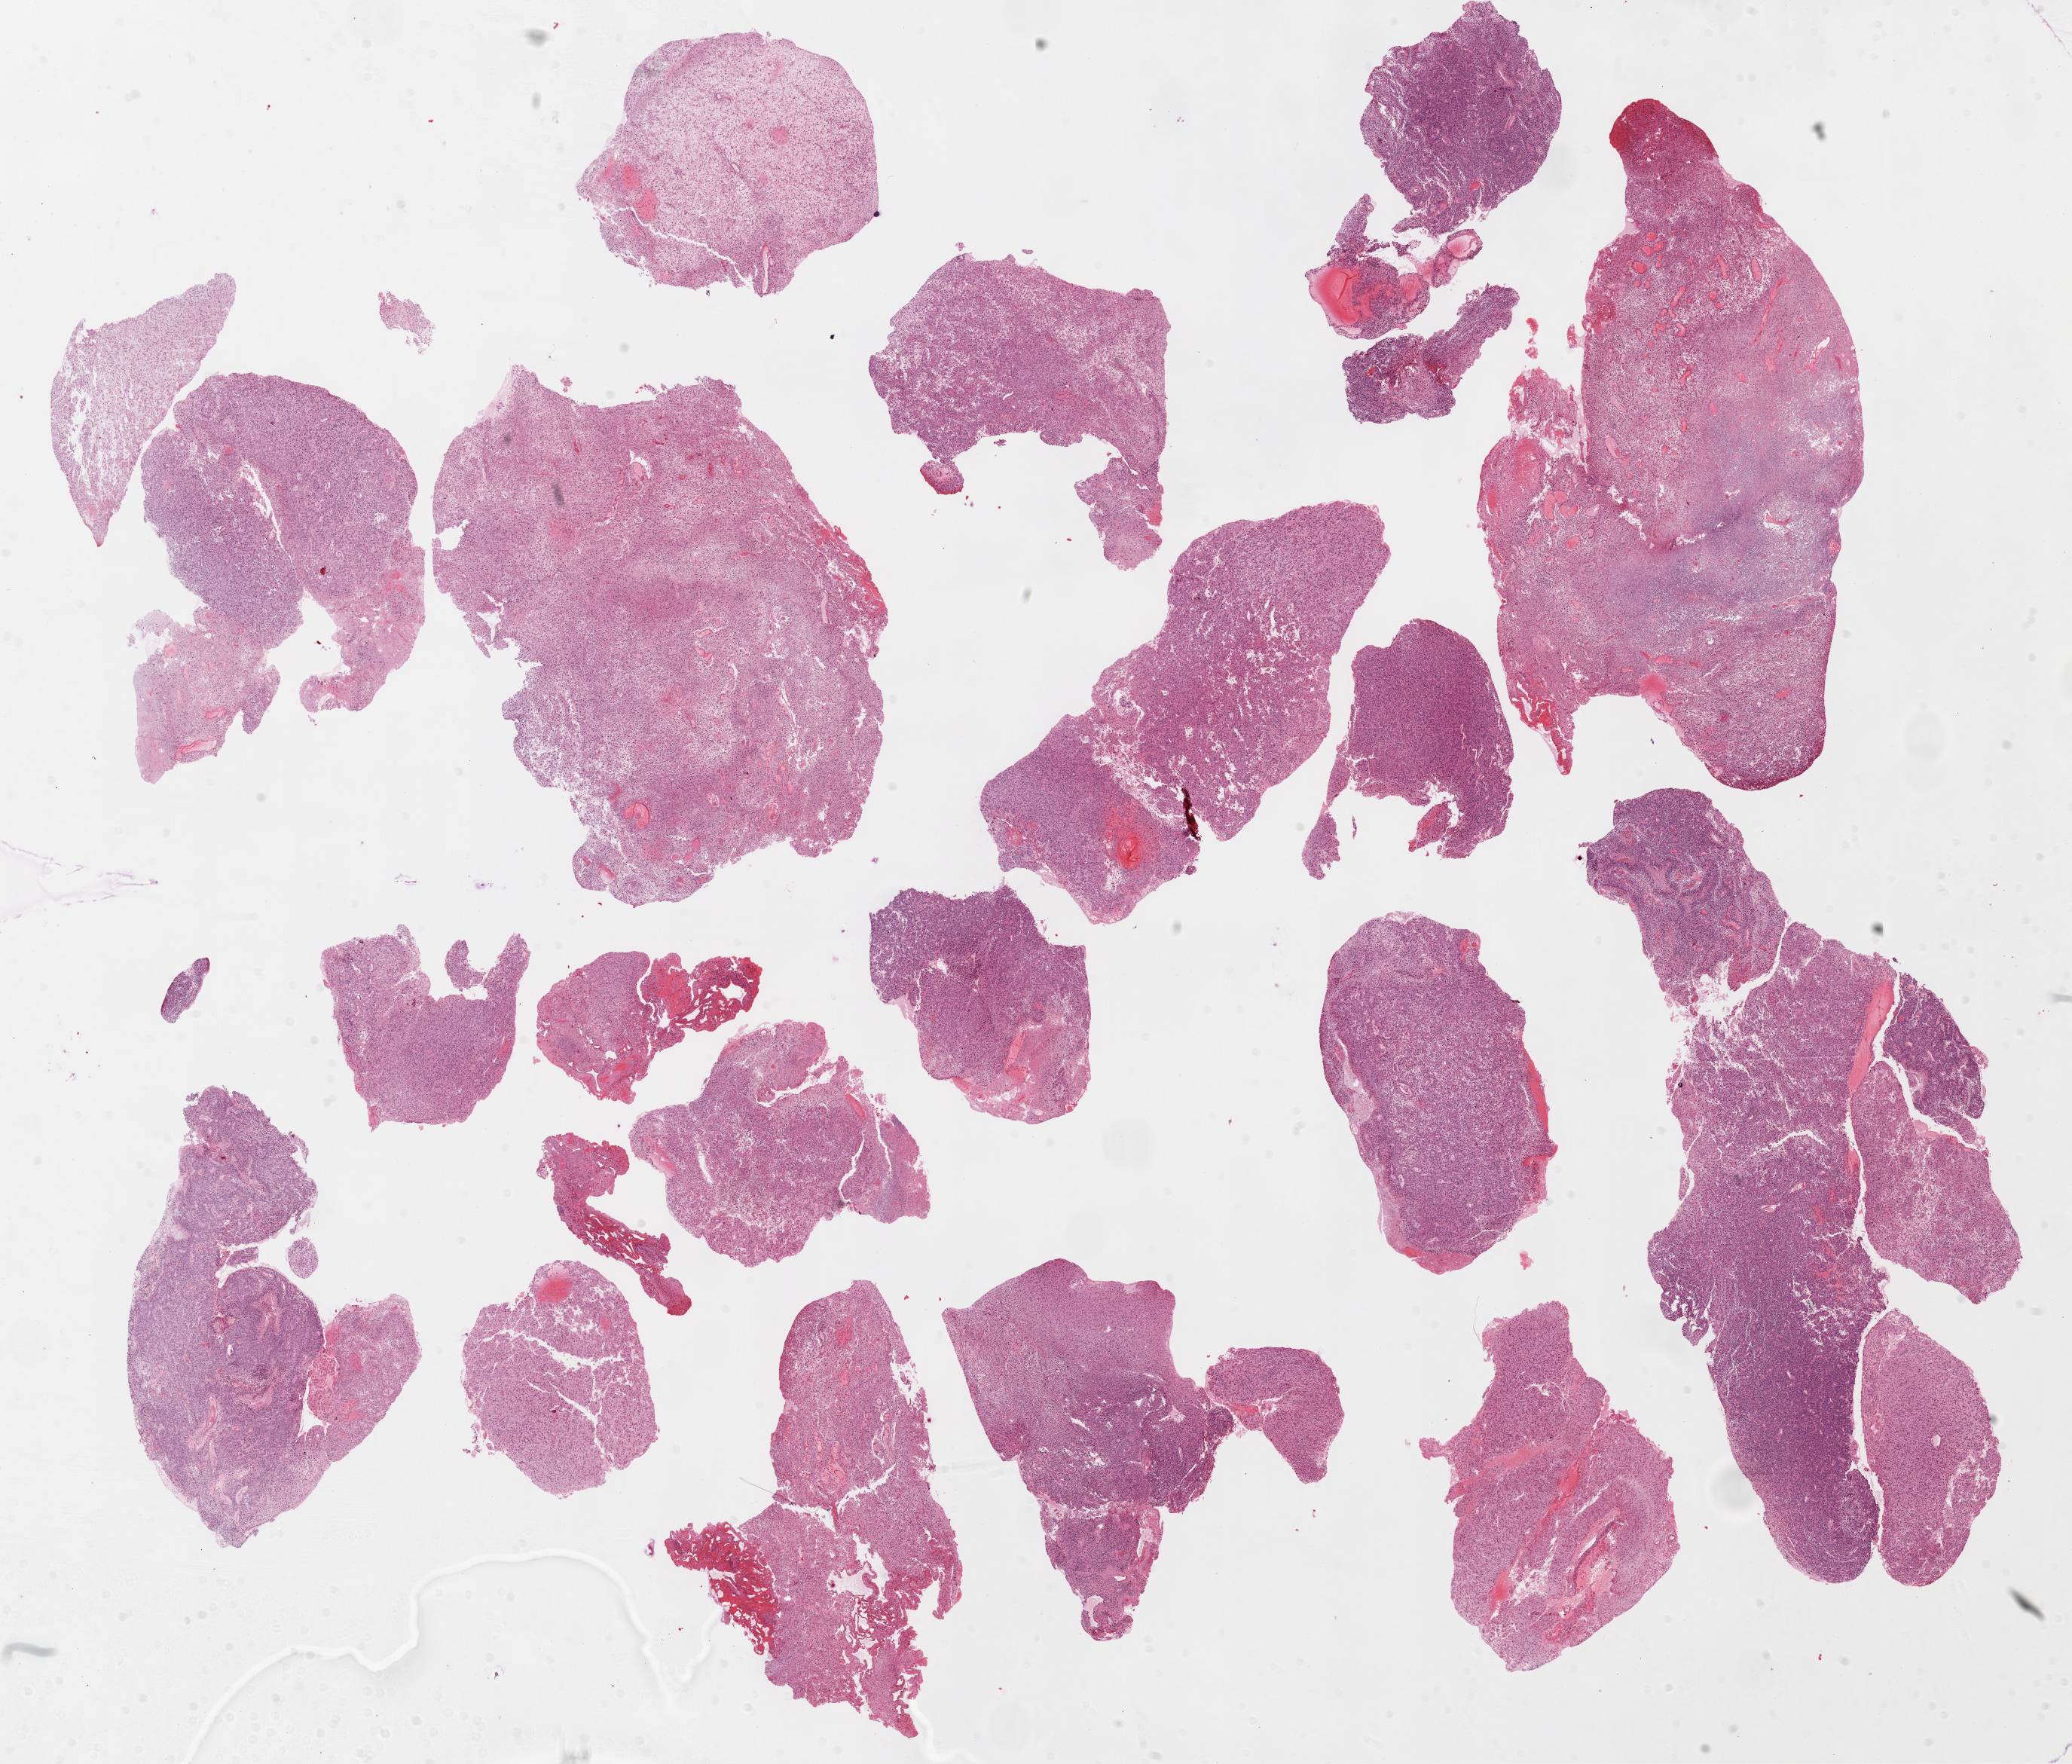
Whole-slide histology image, Hematoxylin and eosin (H&E) stained, shown as a low-resolution overview of the whole scanned area (about 22.1 x 18.8 mm, from a 20x scan), FFPE section, sample: primary tumour, brain. Patient: female, age at initial diagnosis 59 years.
Diagnosis: Glioblastoma.